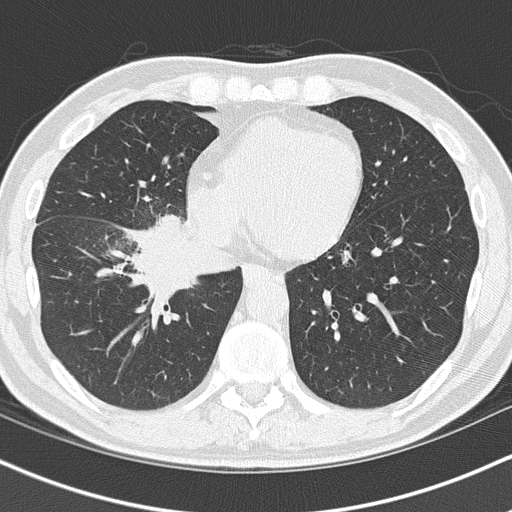
Low-dose screening chest CT, axial slice; first (baseline) screen; lung window (W 1500 / L -600 HU); 120 kVp; slice 46 of 151 in the series. Male participant, aged 55 years at enrolment. Current smoker at enrolment.
Lesion marked by an expert reader, box from (x=126, y=224) to (x=242, y=312) px. Screening reader's record for this exam (one nodule recorded; not confirmed to be the boxed lesion): non-calcified nodule or mass ≥4 mm, right lower lobe, 6 × 5 mm, spiculated (stellate) margins, soft tissue attenuation. Later outcome: lung cancer diagnosed 21 days after this screen — carcinoma, NOS, right hilum, stage IB (AJCC 6th edition), 67 mm at pathology.